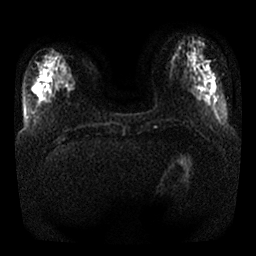
Breast MRI, one axial slice. Position 9 of 32 along the scan axis. Diffusion-weighted series; image 2 of 4 stored at this slice position (different b-values; order by instance number). 1.5 T. 4 mm slice thickness. 256 × 256 image matrix, field of view 350 × 350 mm. Female patient.
Annotated regions visible in this slice (outlined manually by an expert reader):
- tumour on diffusion-weighted imaging: box from (x=59, y=74) to (x=72, y=85) px